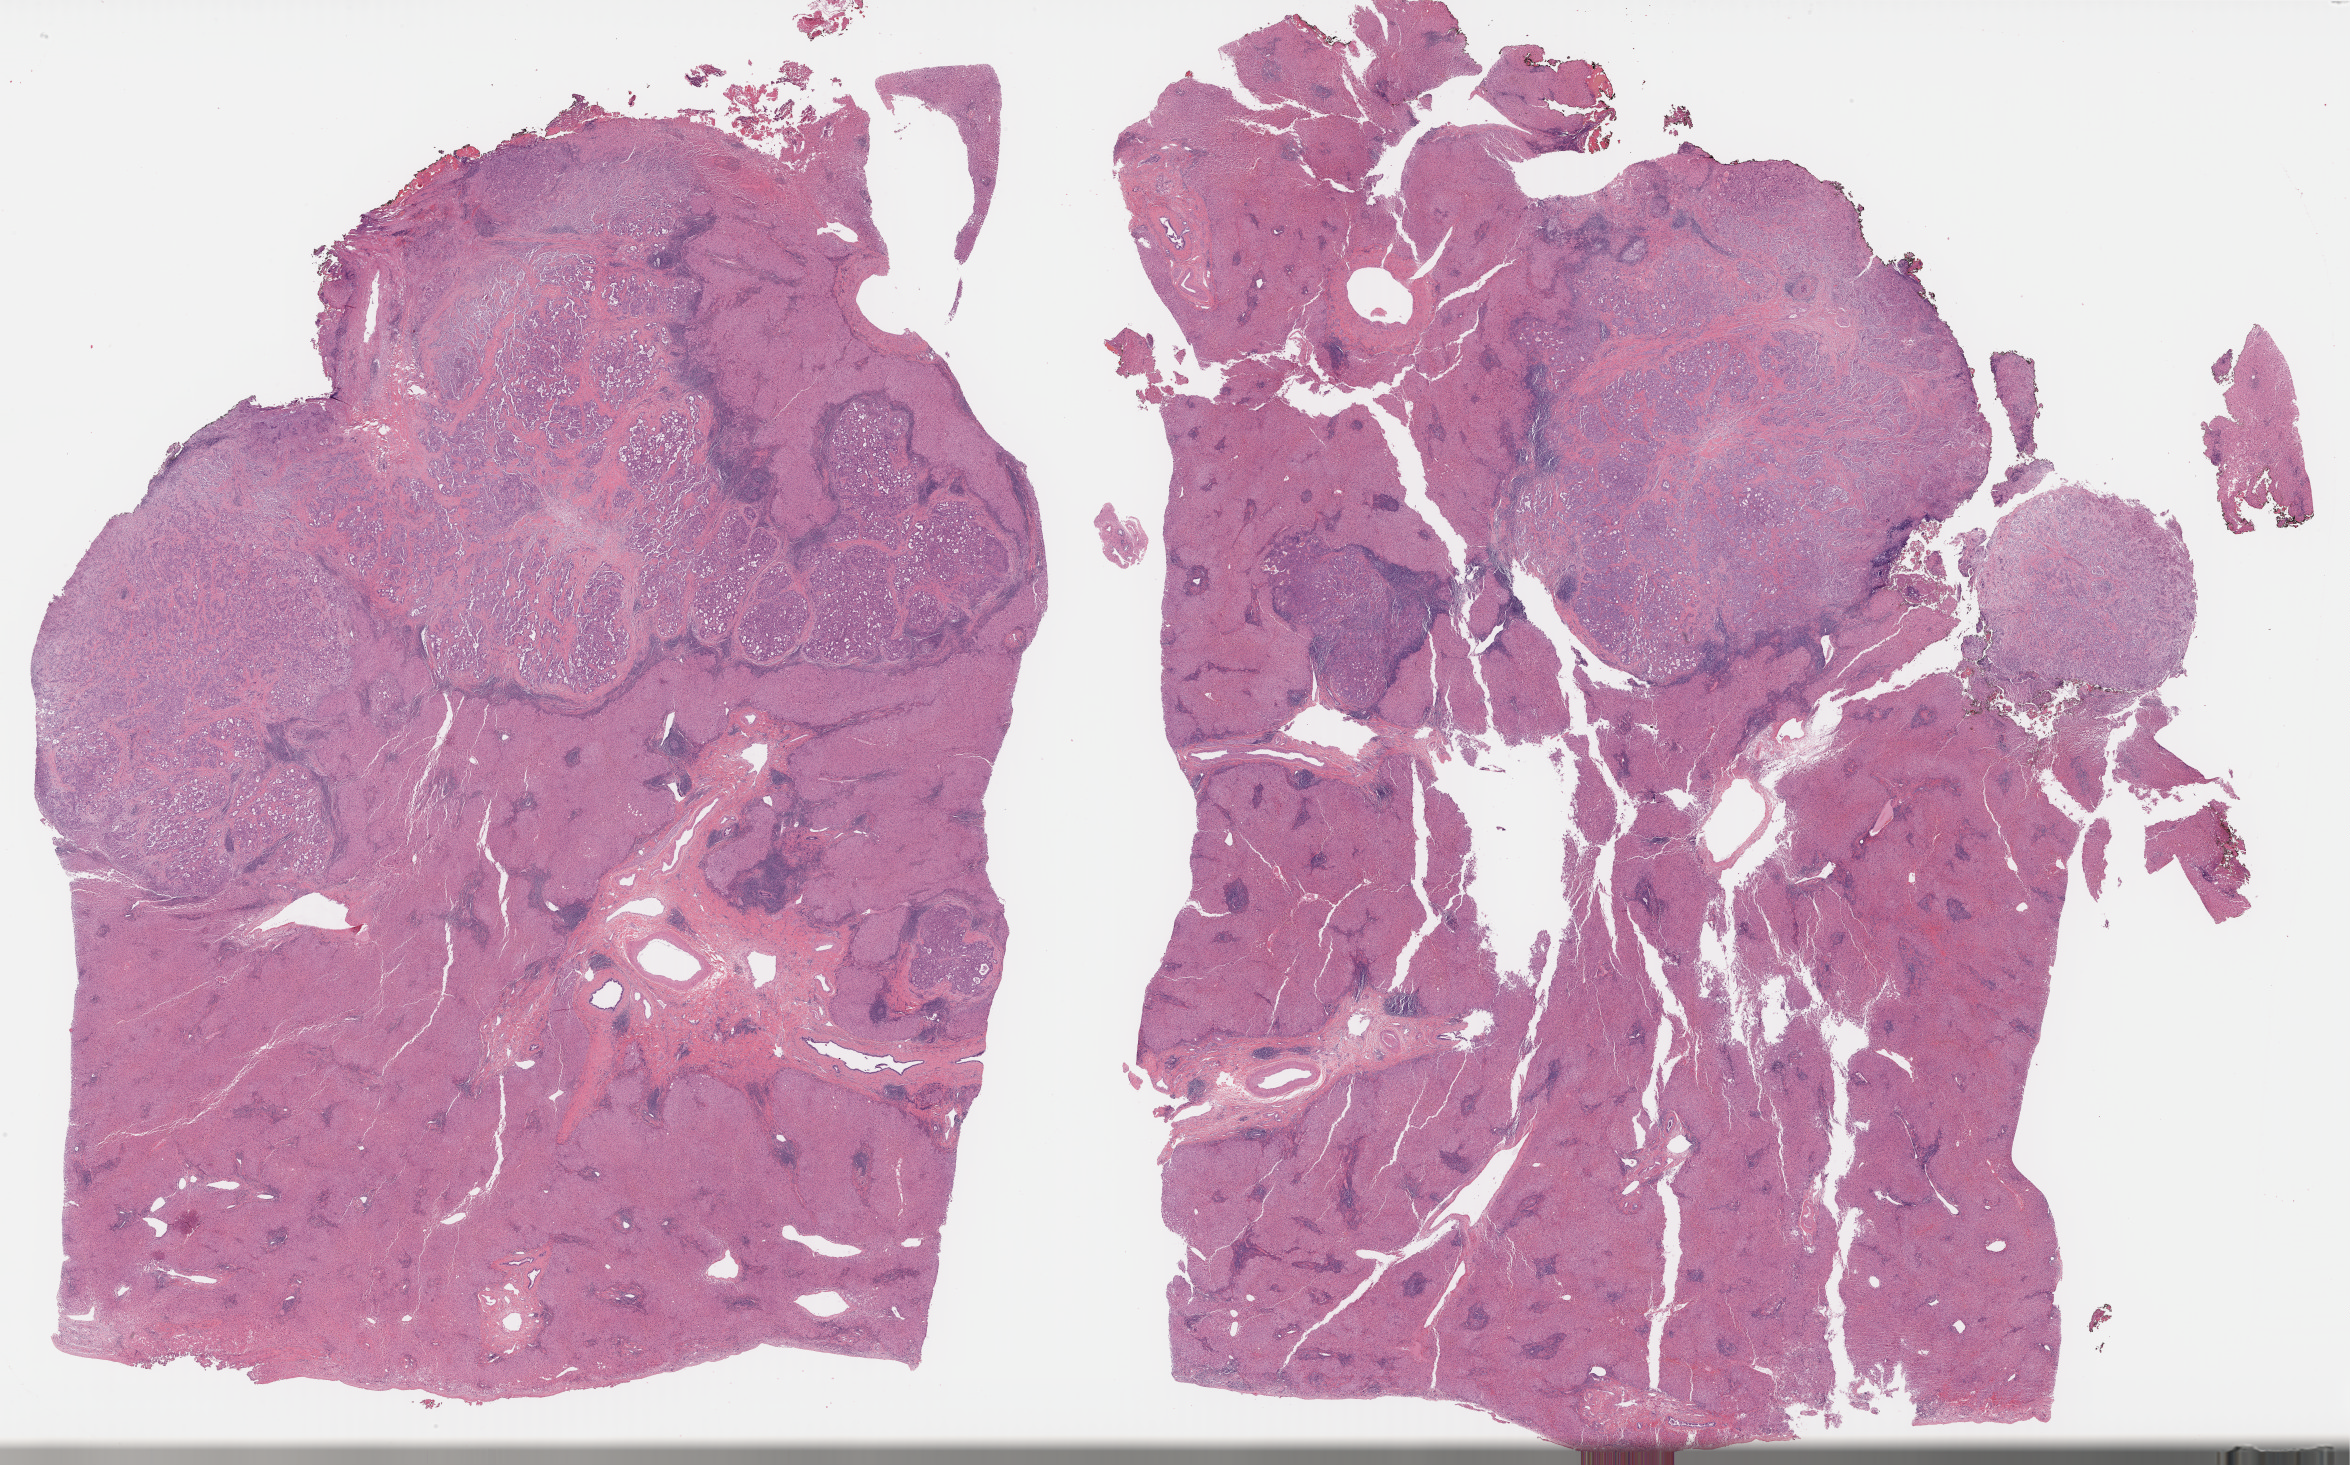
H&E-stained whole-slide image, a low-resolution overview of the entire scanned area, about 38.0 x 23.7 mm; FFPE section; primary tumour sample from the bile duct. Patient: male, age at initial diagnosis 60 years. Histologic grade: G3 (poorly differentiated).
- pathologic diagnosis: Cholangiocarcinoma (intrahepatic bile duct)
- AJCC pathologic stage: I (7th edition)